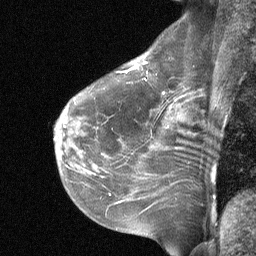
Breast MRI (dynamic contrast-enhanced), one sagittal slice. Slice 41 of 64 in the series (ordered by position). Dynamic contrast-enhanced study with each time point stored as its own series, time point 2 of 3 at this slice position (early post-contrast, ordered by acquisition time). 1.5 T. TE 4.8 ms, TR 27 ms. 256 × 256 image matrix, field of view 200 × 200 mm. Patient: female, 51 years. From the clinical record (not read from this slice): setting: breast cancer imaged before/during neoadjuvant chemotherapy; receptor status: HR-positive, HER2-negative.
Outlined on this slice (semi-automatic segmentation, software-assisted and operator-edited):
- analysis volume of interest (the breast-tissue region the enhancement analysis was run in; not a lesion): bounding box (x1, y1, x2, y2) in pixels: (88, 42, 196, 119)
- tumour enhancement mask (voxels above the 90 % enhancement threshold inside the analysis volume of interest): (134, 63, 144, 68)